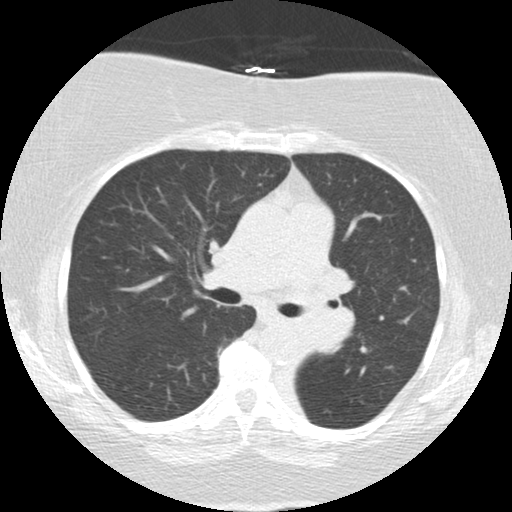
Low-dose screening chest CT, one axial slice; position 81 of 136 along the scan axis; reconstruction kernel STANDARD; lung window (W 1500 / L -600 HU); 2.5 mm slice thickness; 512 × 512 image matrix, field of view 309 × 309 mm.
Outlined on this slice (outlined manually by an expert reader):
- lesion 2 (tumor, mediastinum): box from (x=292, y=266) to (x=354, y=352) px